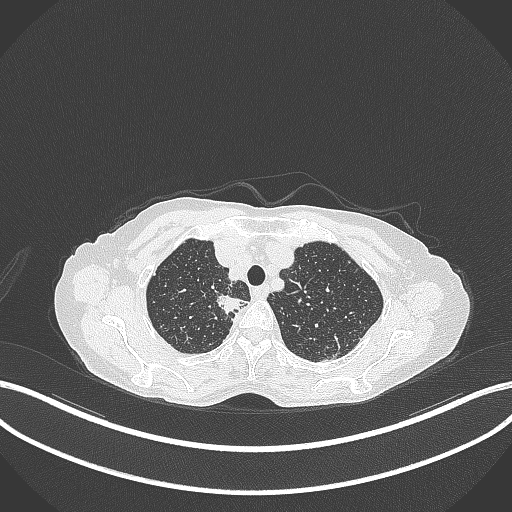
Chest CT, one axial slice. Position 311 of 403 along the scan axis. Reconstruction kernel B70f. Lung window (W 1500 / L -600 HU). 1 mm slice thickness. 512 × 512 image matrix, field of view 400 × 400 mm. Patient: female, 75 years. From the clinical record (not read from this slice): clinical TNM (as recorded): T1c N1 M1.
Structures marked on this image (bounding box drawn by a radiologist):
- lung tumour (recorded histology: adenocarcinoma): bounding box <213,292,247,318> (left, top, right, bottom; pixels)